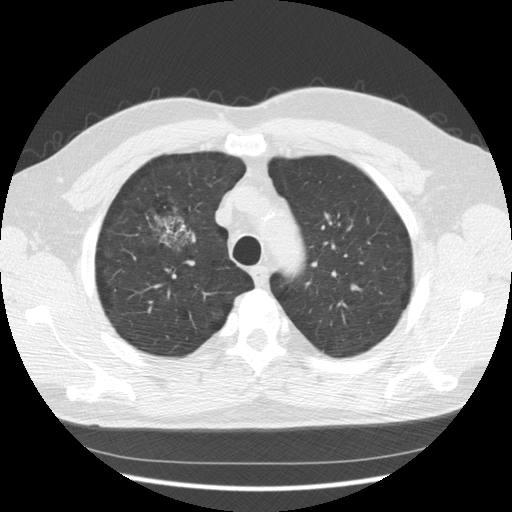
Axial slice from a low-dose chest CT screening exam; third annual screen; lung window (W 1500 / L -600 HU); standard (soft-tissue) reconstruction kernel (STANDARD); 140 kVp. Male participant, aged 60 years at enrolment. Former smoker at enrolment.
Lesion marked by an expert reader, bounding box [x1, y1, x2, y2] px = [141, 203, 200, 267]. Reader record for this screening exam (exam-level; its link to the box is not recorded): non-calcified nodule or mass ≥4 mm, right upper lobe, poorly defined margins, mixed attenuation, pre-existing on the prior screen: yes; interval growth: yes. Lung cancer was diagnosed 121 days after this screen: papillary adenocarcinoma, NOS, right upper lobe, moderately differentiated (G2), stage IB (AJCC 6th edition), 32 mm at pathology.